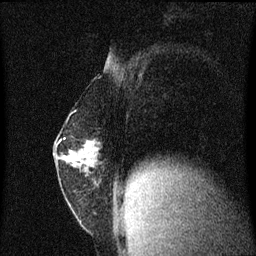
Breast MRI (dynamic contrast-enhanced), one sagittal slice. Slice 26 of 60 in the series (ordered by position). Dynamic contrast-enhanced series, image 2 of 3 at this slice position (ordered by acquisition). 1.5 T. TE 4.2 ms, TR 8.4 ms. 2 mm slice thickness. 256 × 256 image matrix, field of view 200 × 200 mm. Patient: female, 52 years. Case-level facts recorded for this patient, not image findings: setting: breast cancer imaged before/during neoadjuvant chemotherapy; receptor status: HER2-positive.
Outlined on this slice (semi-automatically segmented with operator editing):
- analysis volume of interest (the breast-tissue region the enhancement analysis was run in; not a lesion): bounding box [x1, y1, x2, y2] px = [54, 124, 119, 191]
- tumour enhancement mask (voxels above the 70 % enhancement threshold inside the analysis volume of interest): [70, 142, 88, 157]